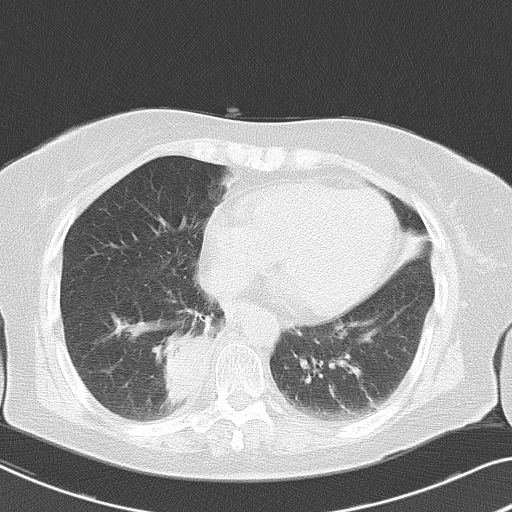
Chest CT, one axial slice. Position 18 of 53 along the scan axis. Lung window (W 1500 / L -600 HU). 512 × 512 image matrix. Female patient, age 70 years. Case-level facts recorded for this patient, not image findings: clinical TNM (as recorded): T2 N1 M1a.
Outlined on this slice (rectangle marked by the reading radiologist):
- lung tumour (recorded histology: adenocarcinoma): box from (x=156, y=318) to (x=213, y=418) px